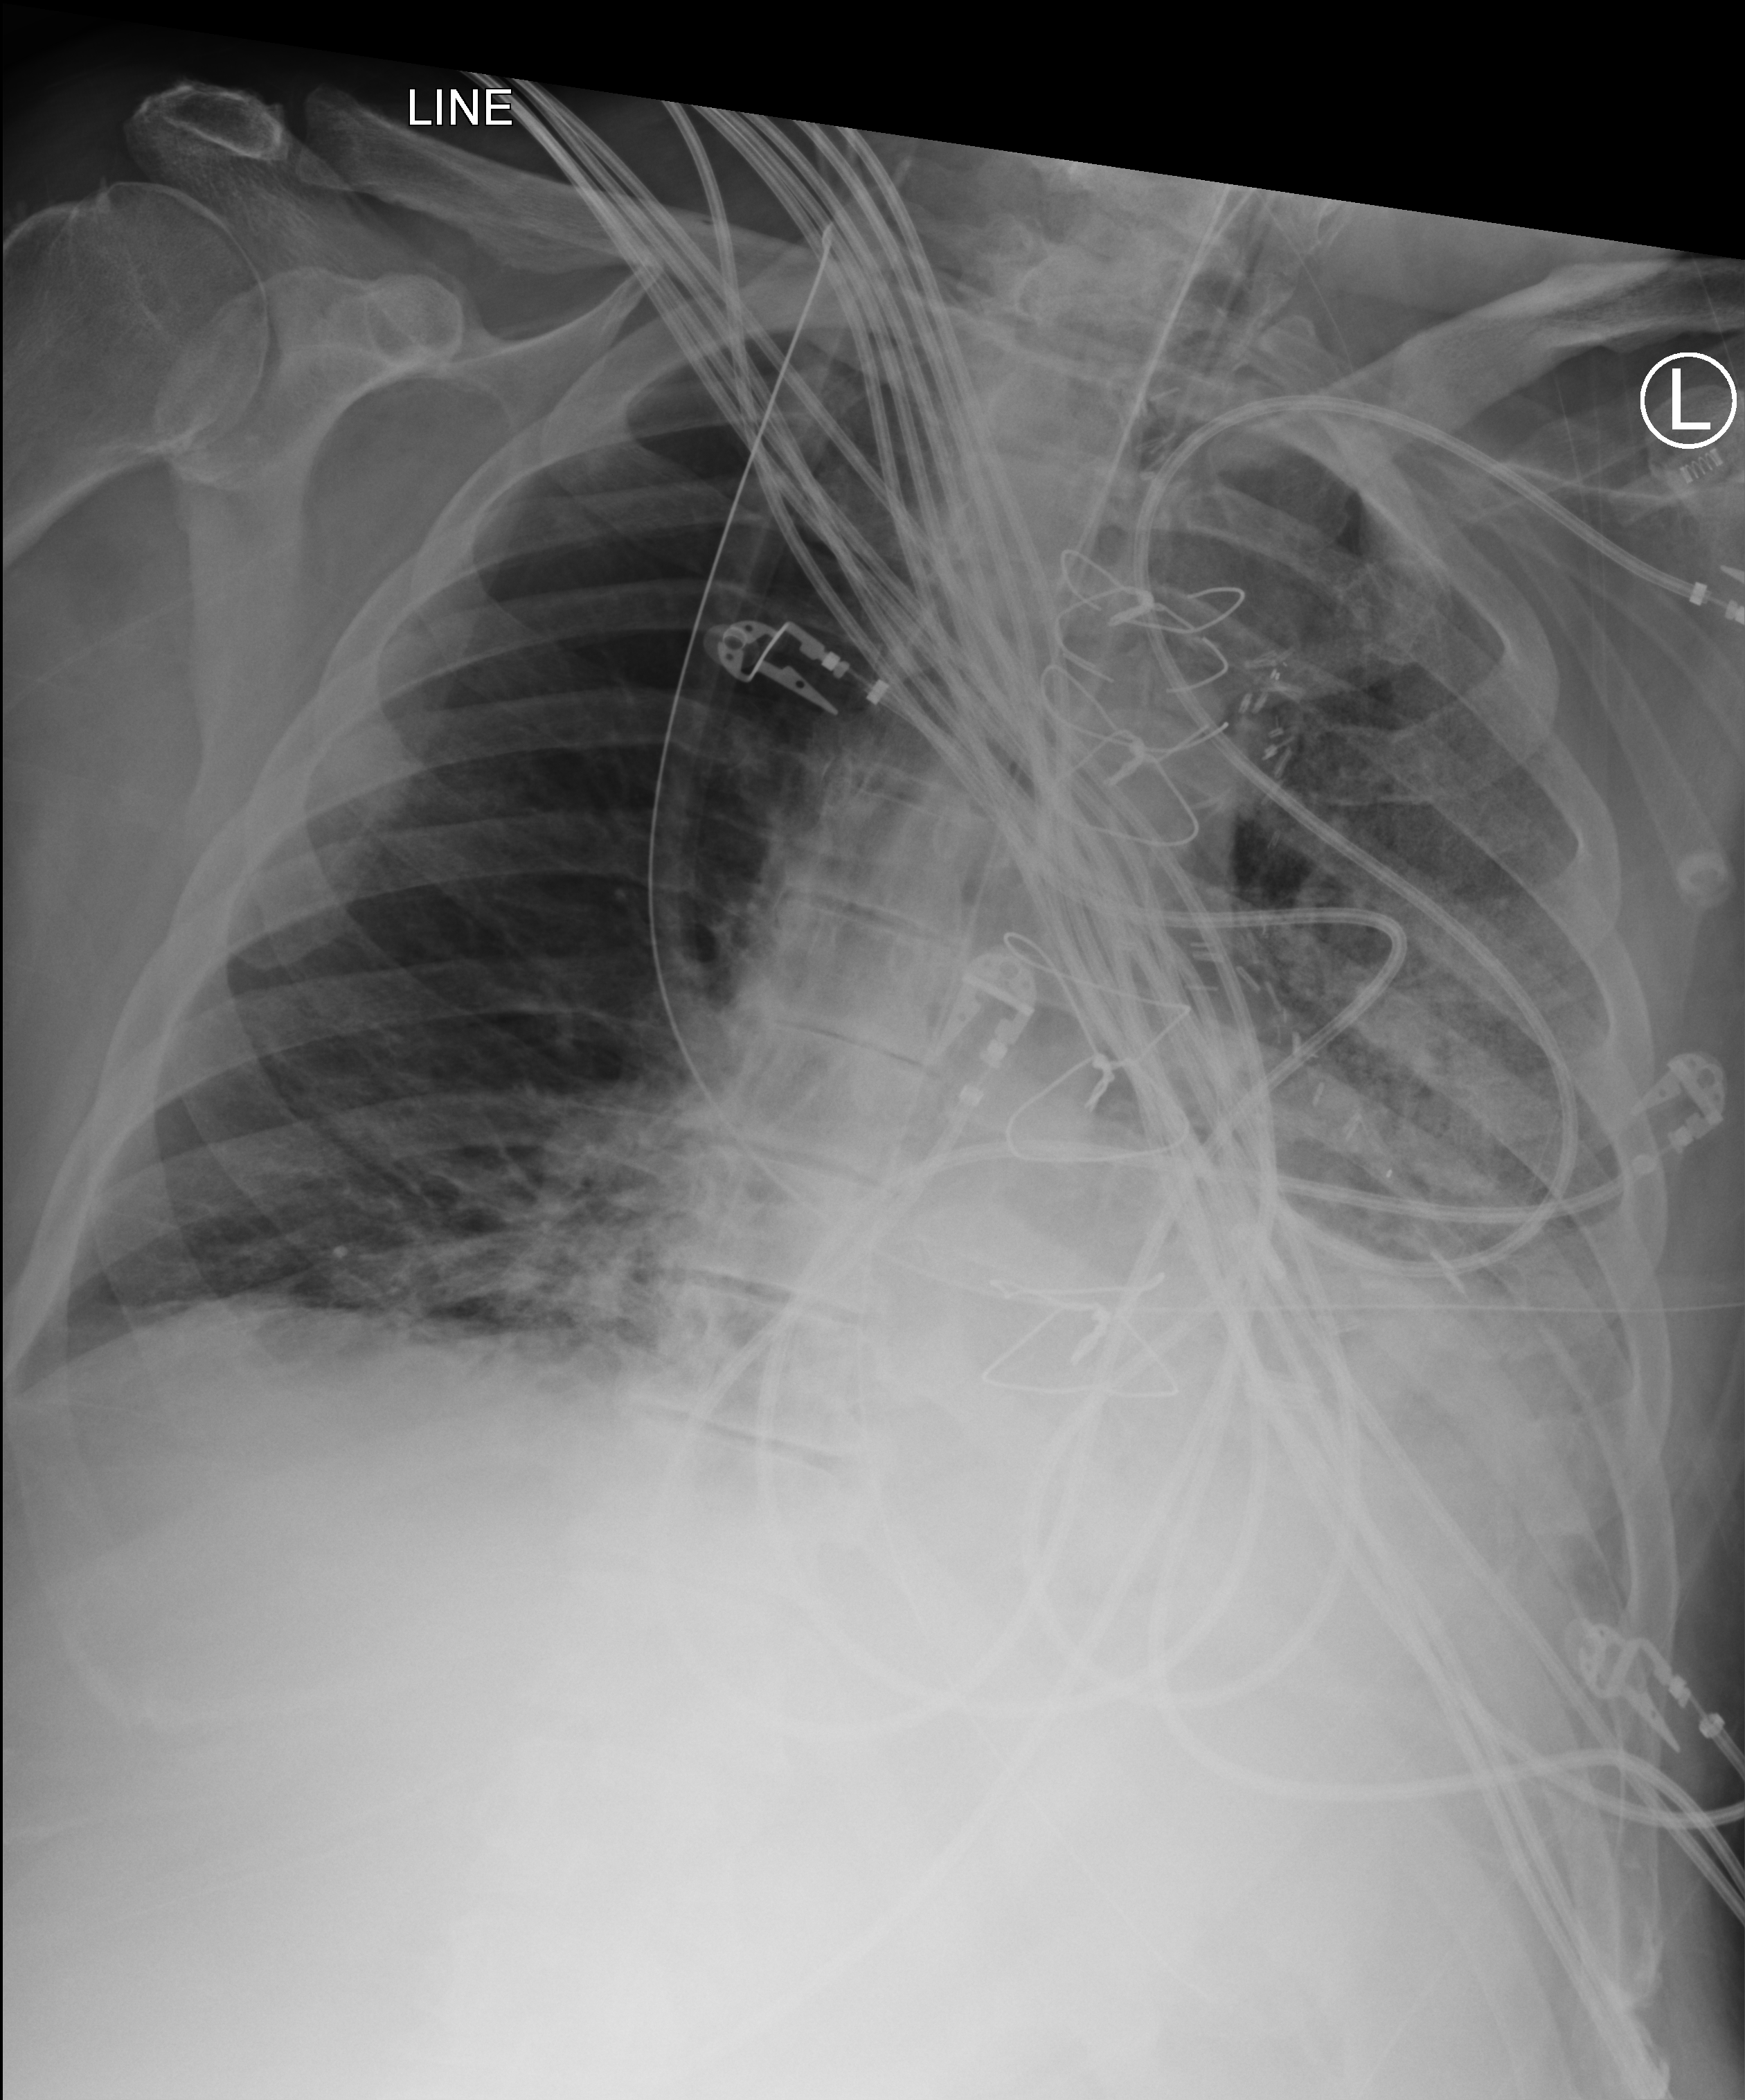
Bedside chest radiograph (computed radiography), anteroposterior (AP) projection. Patient hospitalised with COVID-19; male, aged 60–74 years.
Admission-level facts for this patient (not findings on this image; timing relative to this image not recorded): smoking status (admission record): former; mechanically ventilated during this hospital stay: yes.